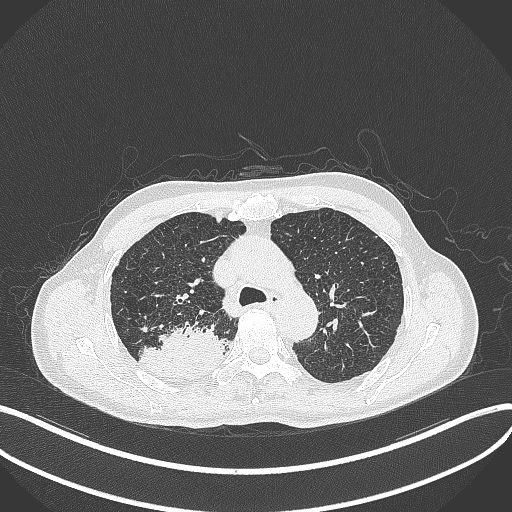
Chest CT, one axial slice. Slice 322 of 428 in the series (ordered by position). Lung window (W 1500 / L -600 HU). 1 mm slice thickness. 512 × 512 image matrix, field of view 400 × 400 mm. Male patient, age 79 years. From the clinical record (not read from this slice): clinical TNM (as recorded): T3 N0 M0.
Annotated regions visible in this slice (bounding box drawn by a radiologist):
- lung tumour (recorded histology: adenocarcinoma): box from (x=136, y=320) to (x=229, y=382) px